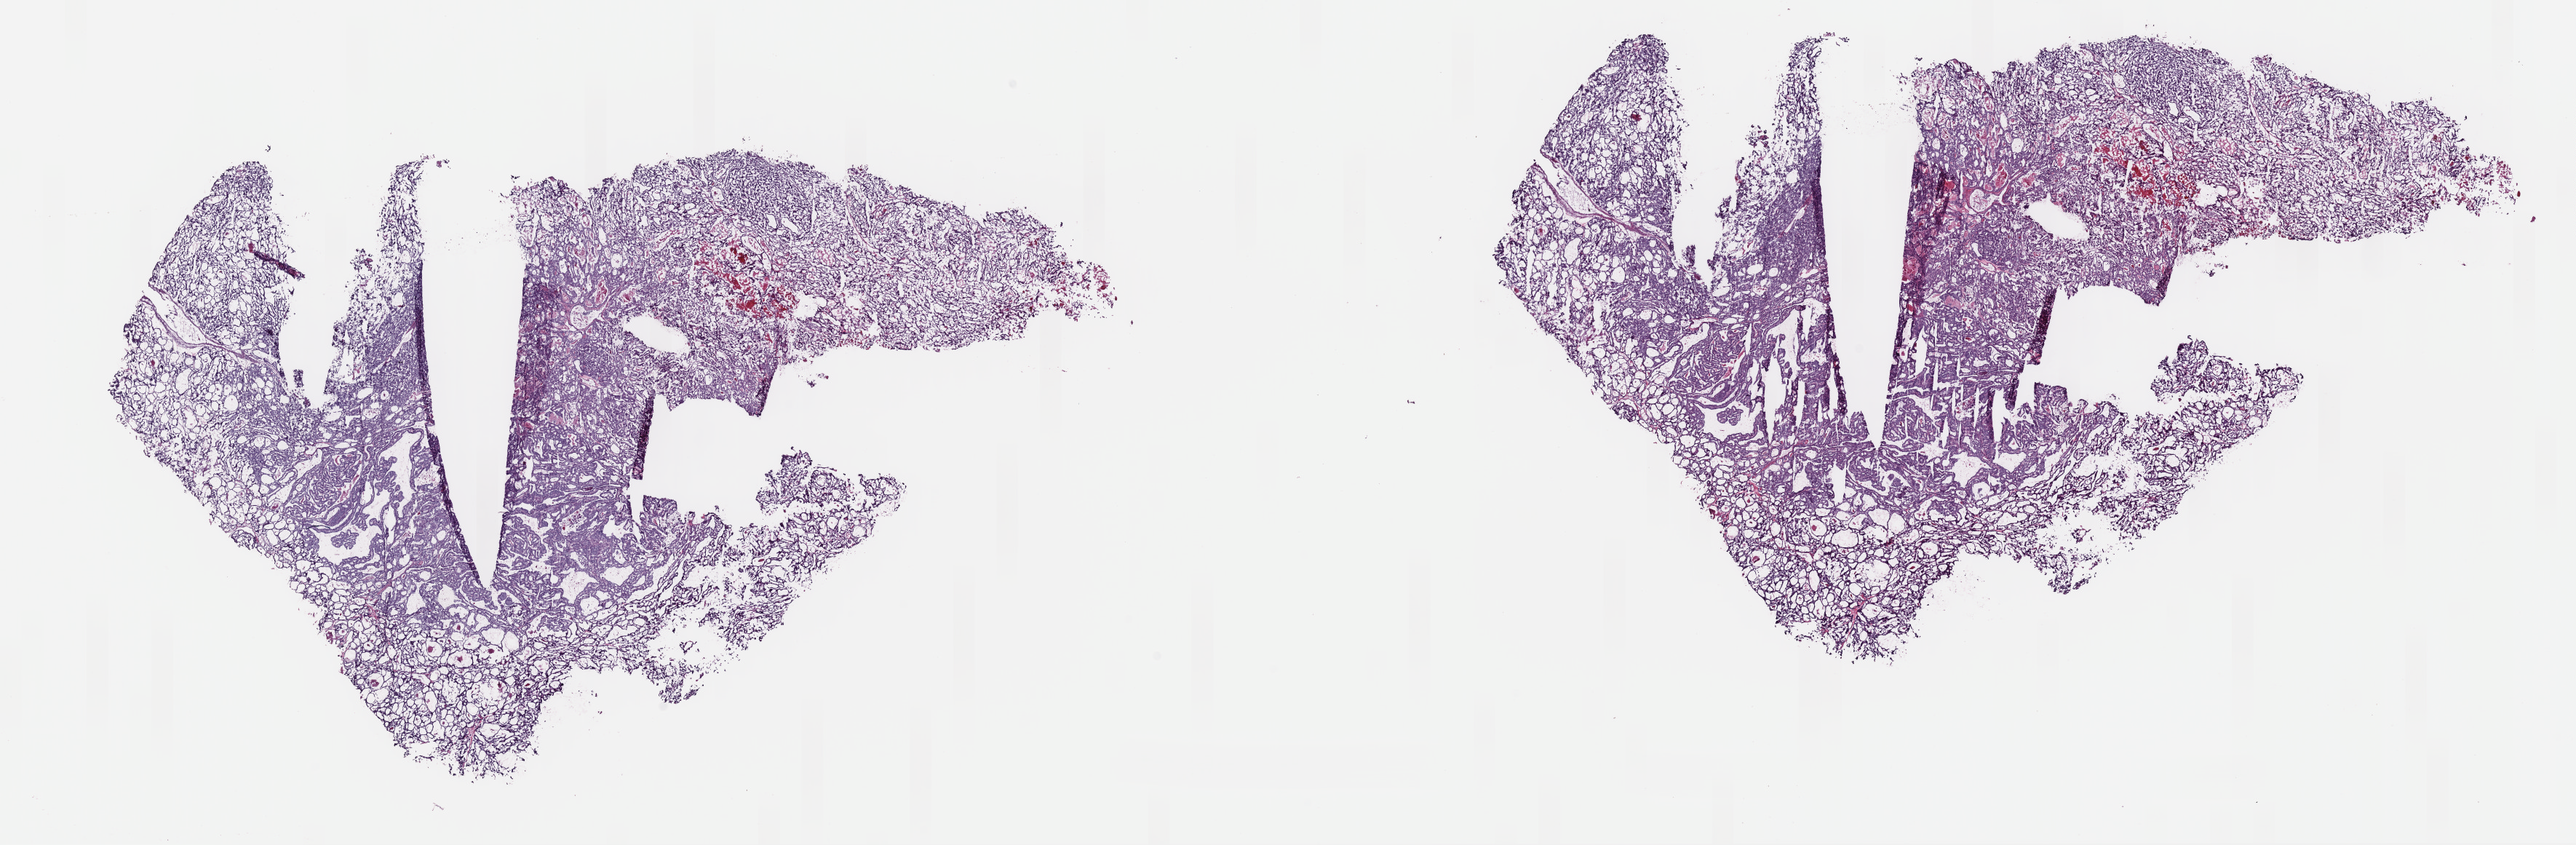
Digitized Hematoxylin and eosin (H&E) stained tissue section (whole slide) — a low-resolution overview of the entire scanned area, about 28.0 x 9.2 mm (from a 40x scan); frozen section from the top of the tissue portion; thyroid, primary tumour sample. Female, age 55 years at initial diagnosis.
Pathologic diagnosis: Papillary carcinoma, follicular variant (thyroid gland).